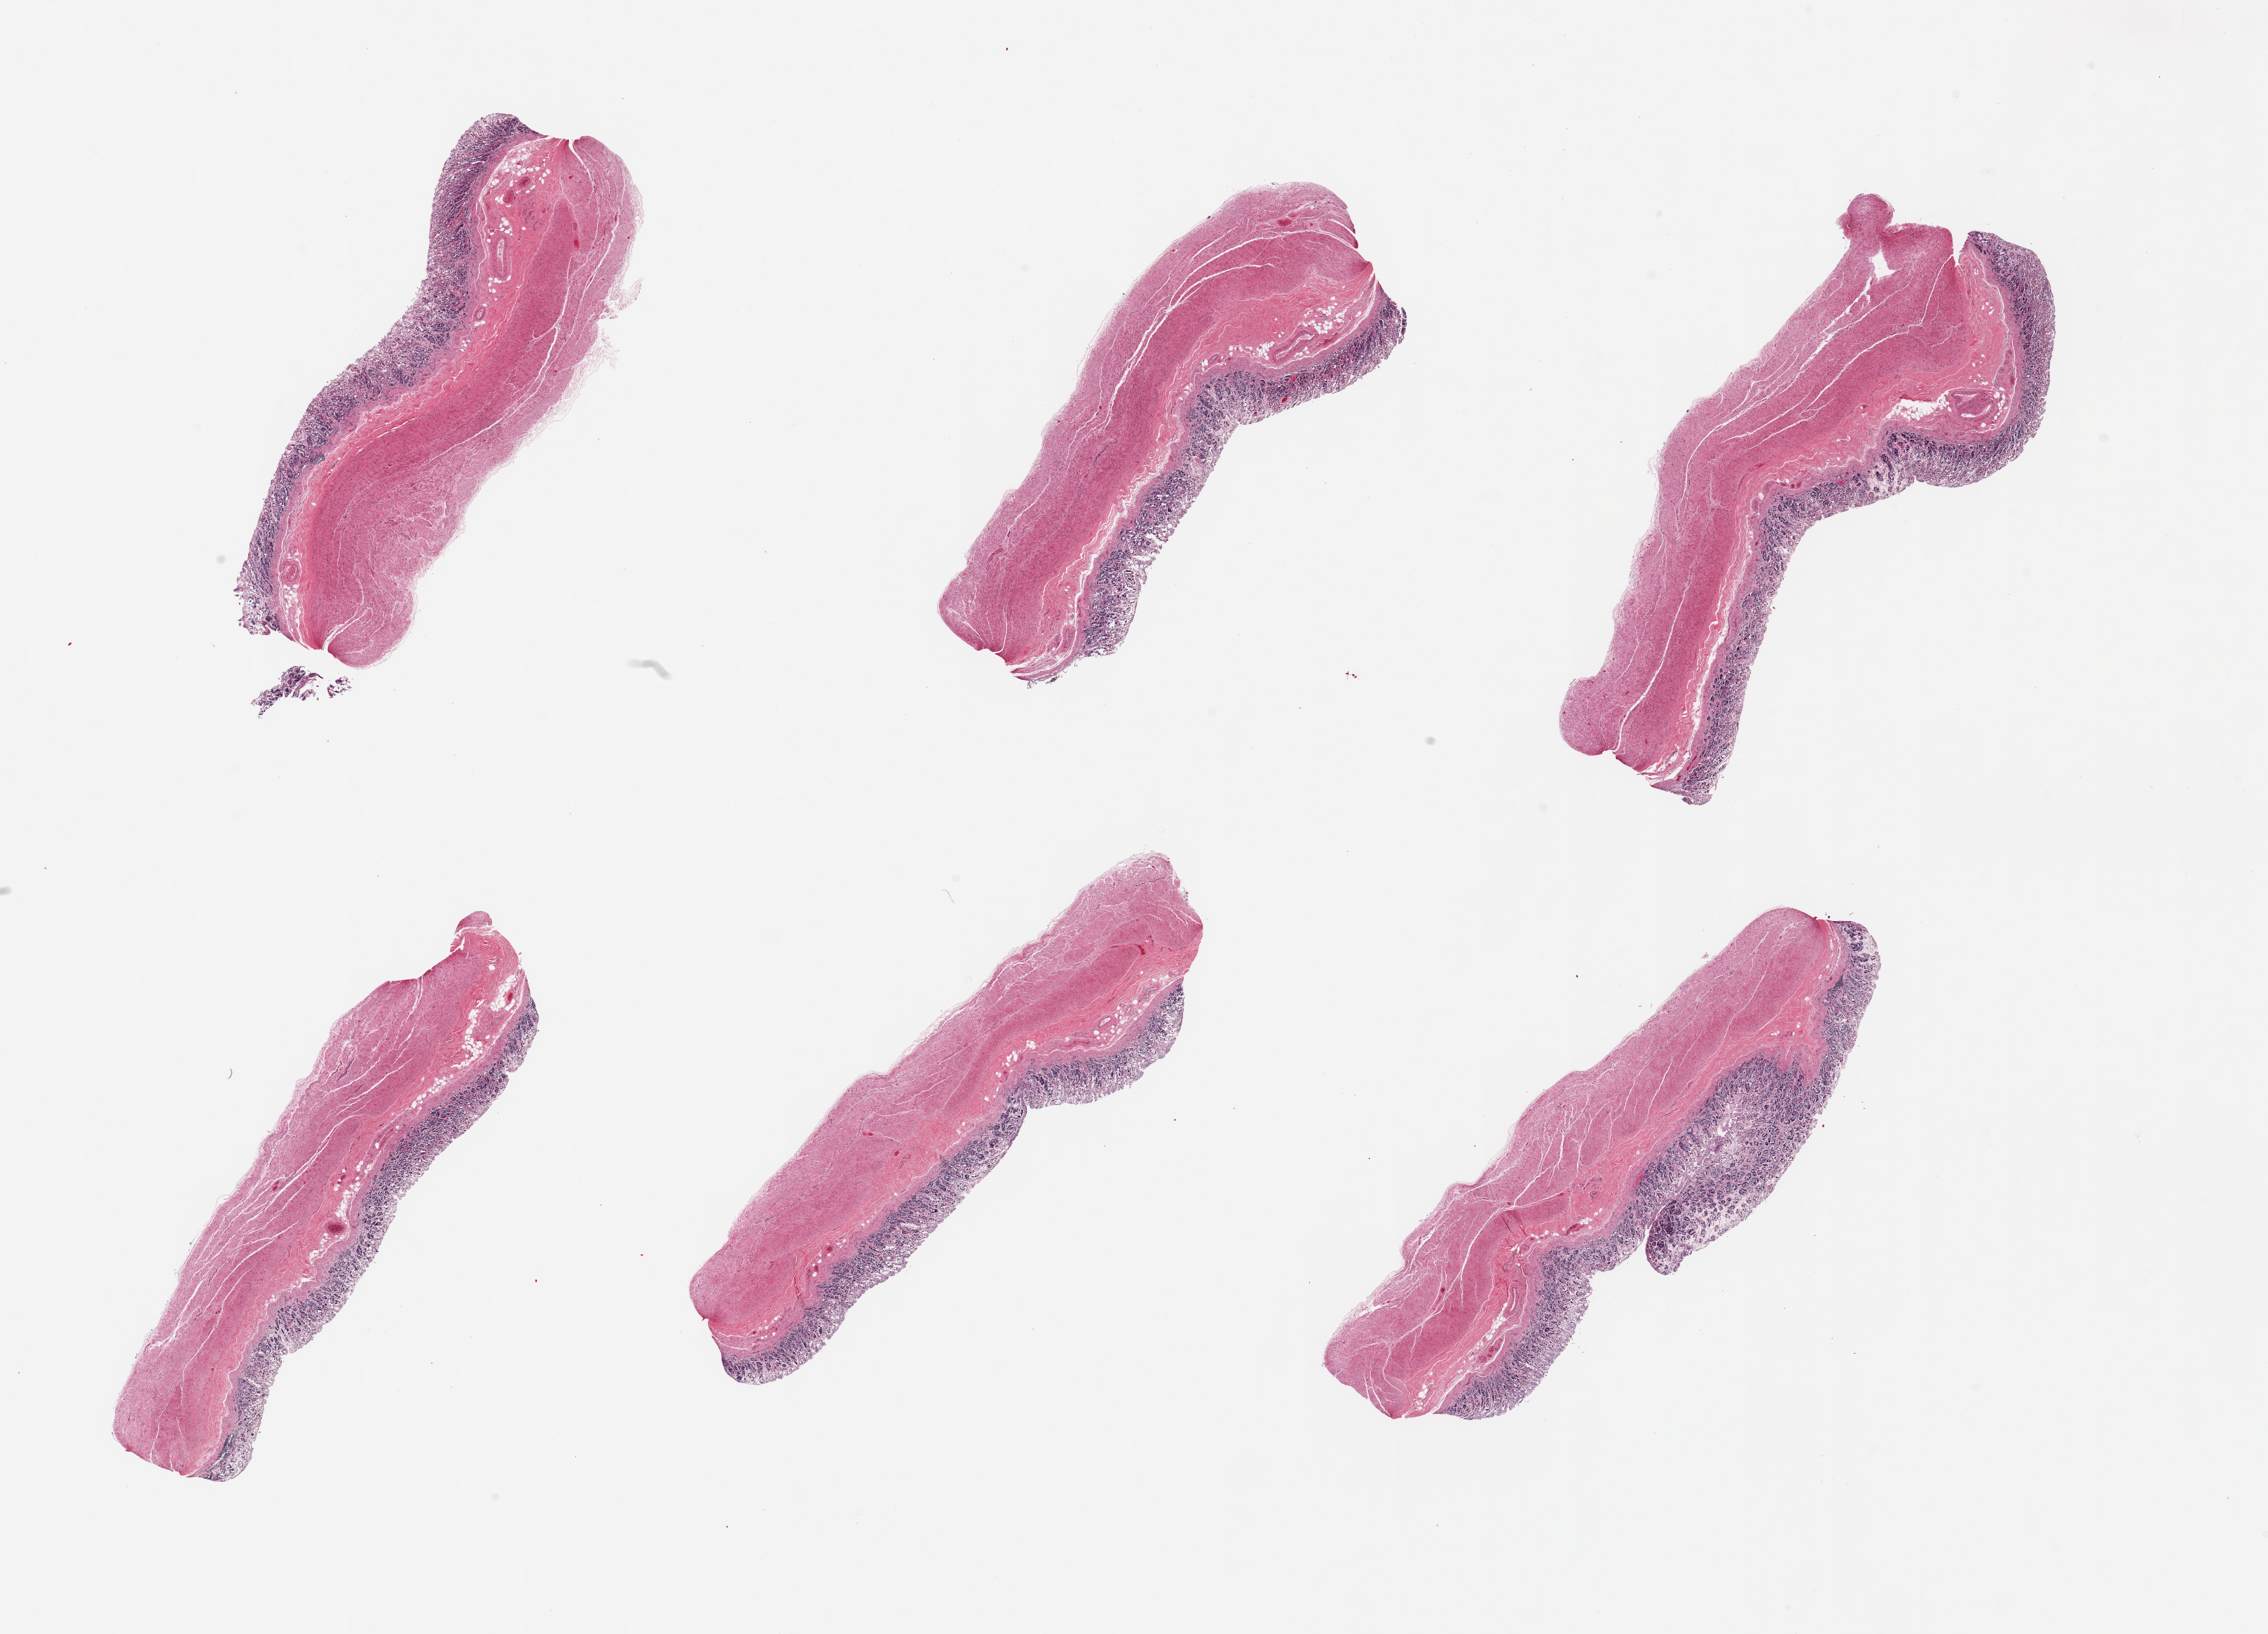
Digitized hematoxylin and eosin (H&E)-stained section — a low-resolution overview of the entire scanned area, about 25.6 x 18.4 mm; PAXgene-fixed paraffin-embedded (PFPE) section; sampled site (target tissue): stomach; tissue donor sample. Donor: male.
Pathologist's review note for this sample: 6 pieces, mucosa up to ~0.5mm but with moderate-advanced autolysis.